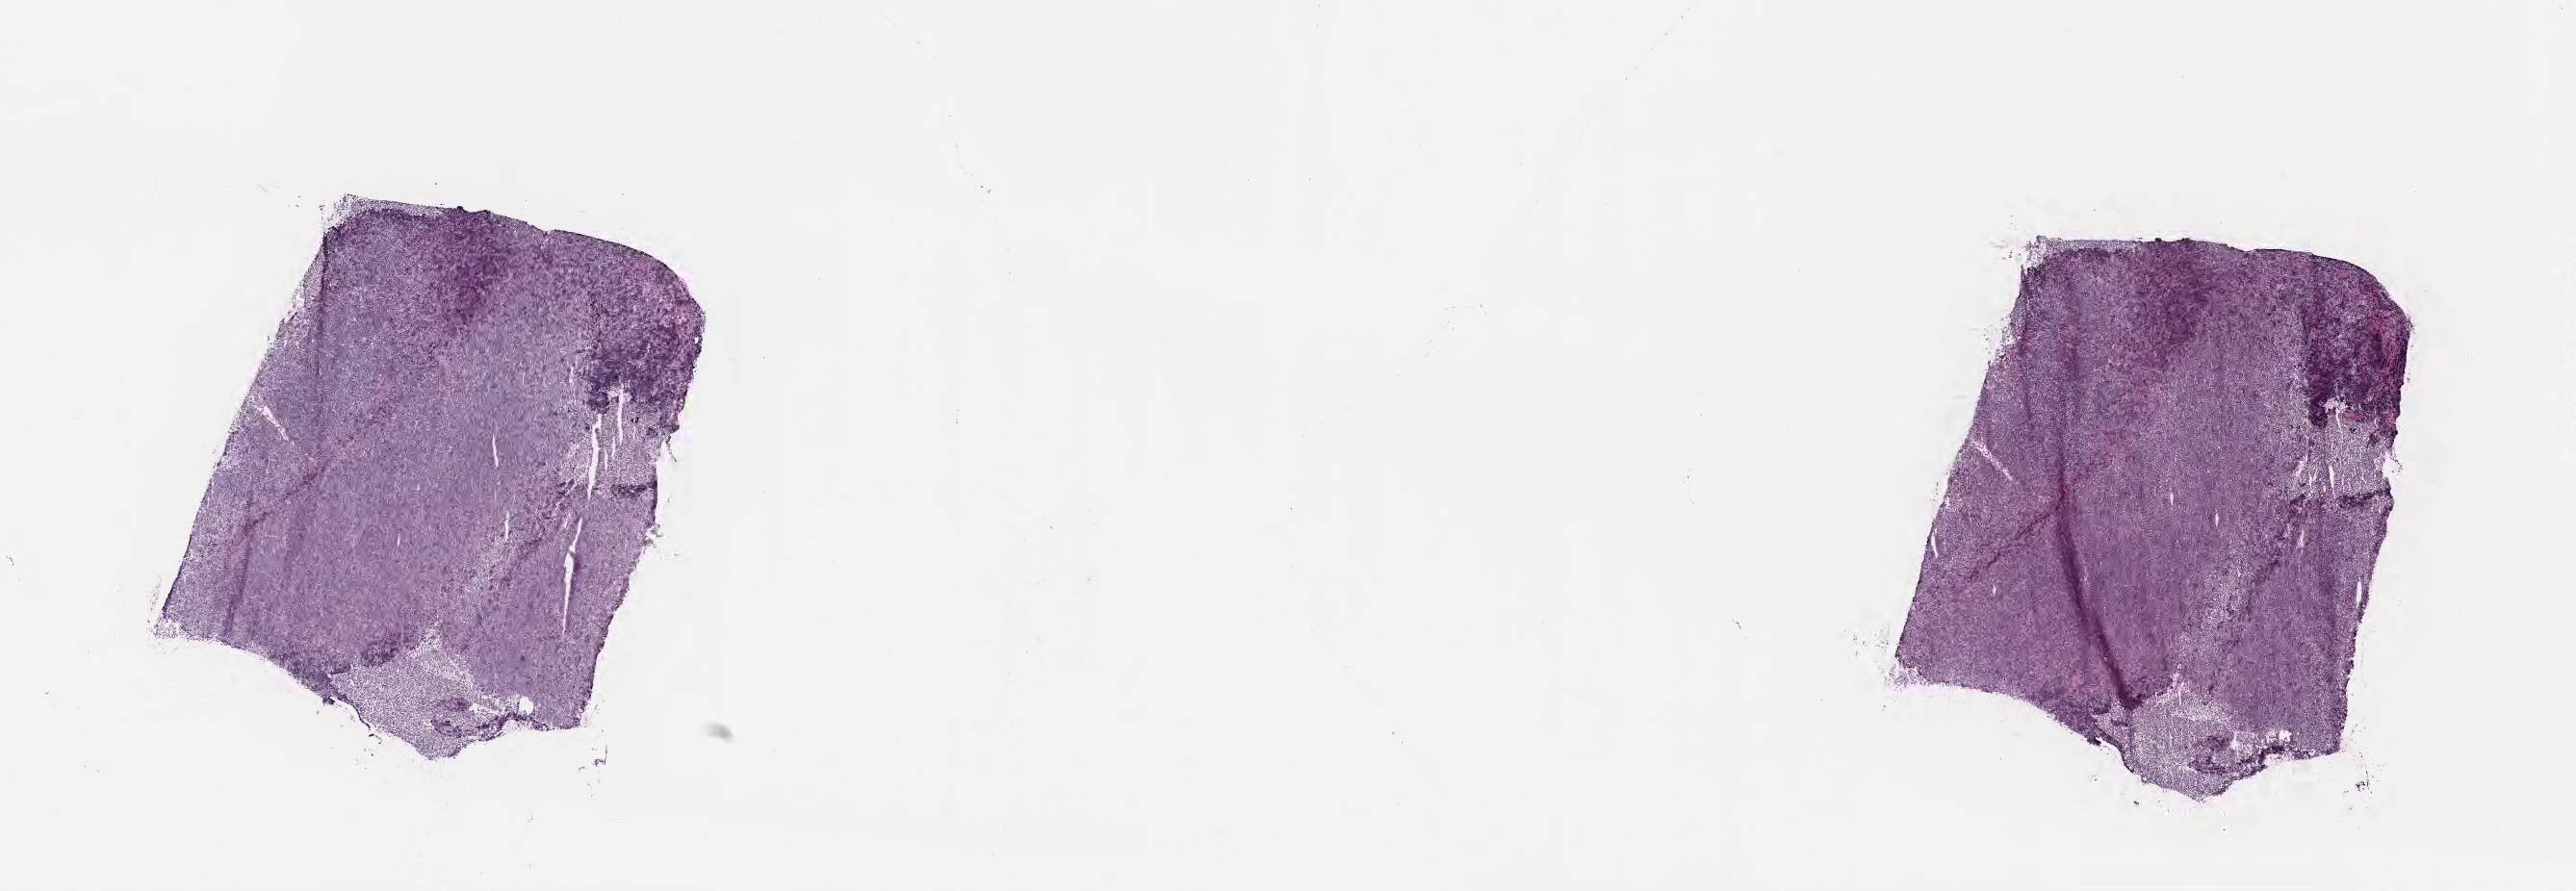
Whole-slide image, H&E stain, shown as a low-resolution overview of the whole scanned area (about 21.6 x 7.5 mm); frozen section (tissue freezing medium); specimen: primary tumor; site: buccal mucosa. Patient: male, age at initial diagnosis 5 years. Composition of this section per pathologist review: tumor cells 90%, tumor nuclei 95%, stromal cells 5%, necrosis 5%, normal cells 0%. Infiltration values recorded for this section: lymphocyte infiltration 35%, monocyte infiltration 40%, neutrophil infiltration 5%.
Ann Arbor stage (patient): Stage II. Histologic diagnosis: Diffuse large B-cell lymphoma, NOS.